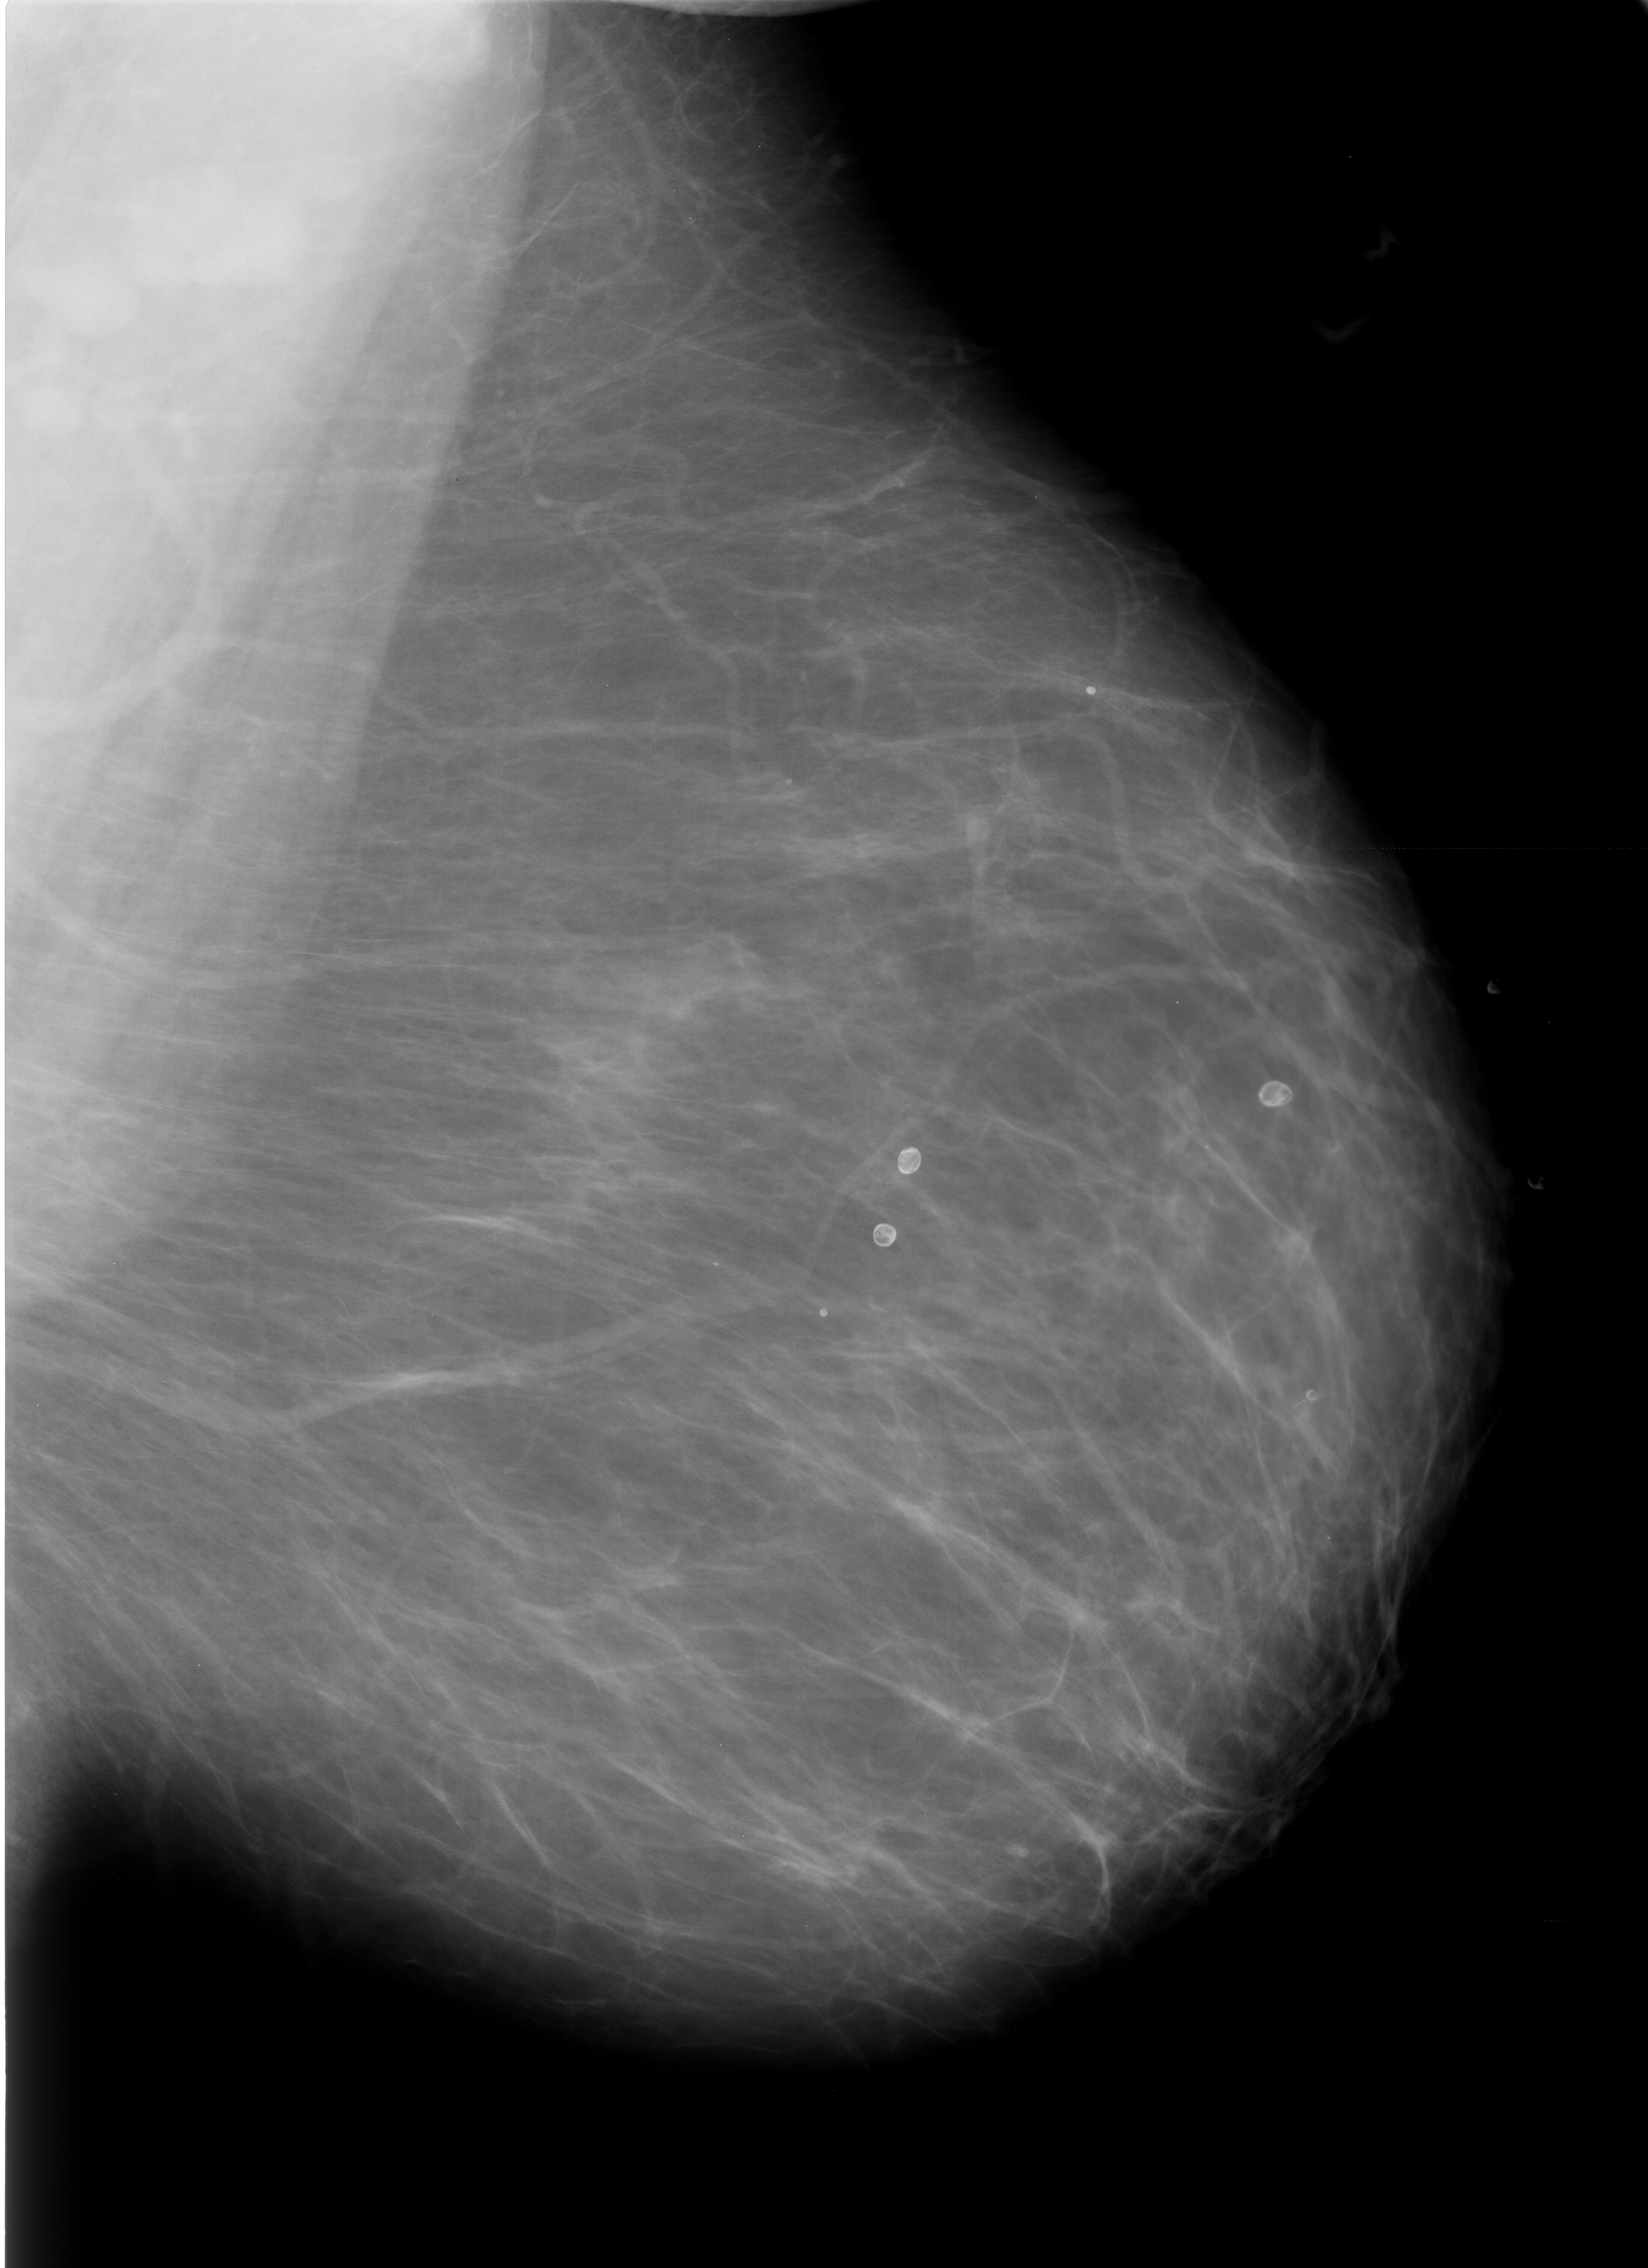
Mammogram (digitized film); left breast; MLO view.
Marked findings (only marked abnormalities are described; nothing is implied about the rest of the image): Finding 1 of 7: calcifications, morphology eggshell; BI-RADS assessment category 2; subtlety rating 5 on a 1 (subtle) to 5 (obvious) scale; benign without callback (not worked up further). Finding 2 of 7: calcifications, morphology lucent center; BI-RADS assessment category 2; subtlety rating 5 on a 1 (subtle) to 5 (obvious) scale; benign; no additional work-up was recommended (benign without callback). Finding 3 of 7: calcifications, morphology lucent center; BI-RADS assessment category 2; benign without callback (not worked up further). Finding 4 of 7: calcifications, morphology lucent center; BI-RADS assessment category 2; benign without callback (not worked up further). Finding 5 of 7: calcifications, morphology lucent center; BI-RADS assessment category 2; benign; no additional work-up was recommended (benign without callback). Finding 6 of 7: calcifications, morphology lucent center; BI-RADS assessment category 2; benign without callback (not worked up further). Finding 7 of 7: calcifications, morphology lucent center; BI-RADS assessment category 2; benign without callback (not worked up further).